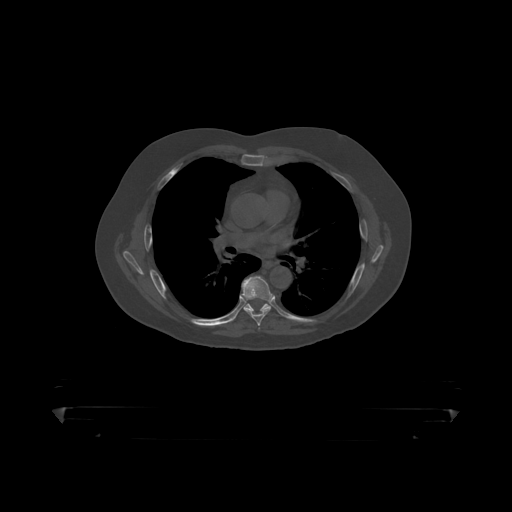
CT including the spine, one axial slice; slice 292 of 390 in the series (ordered by position); reconstruction kernel STANDARD; 120 kVp; bone window (W 1800 / L 400 HU); 512 × 512 image matrix. Patient: male, 60 years. Case-level facts recorded for this patient, not image findings: primary cancer: prostate.
Annotated regions visible in this slice (semi-automatic segmentation, software-assisted and operator-edited):
- T6 vertebra: bounding box [x1, y1, x2, y2] px = [242, 276, 274, 319]
- T7 vertebra: [244, 303, 271, 312]